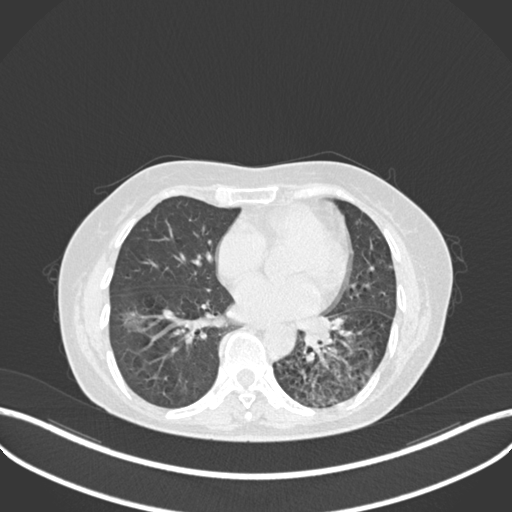
Chest CT, one axial slice. Position 109 of 270 along the scan axis. Reconstruction kernel B30f. Lung window (W 1500 / L -600 HU). 1 mm slice thickness. 512 × 512 image matrix, field of view 400 × 400 mm. Patient: female, 63 years. From the clinical record (not read from this slice): clinical TNM (as recorded): T1b N0 M0.
Outlined on this slice (rectangle marked by the reading radiologist):
- lung tumour (recorded histology: adenocarcinoma): bounding box <292,309,336,357> (left, top, right, bottom; pixels)